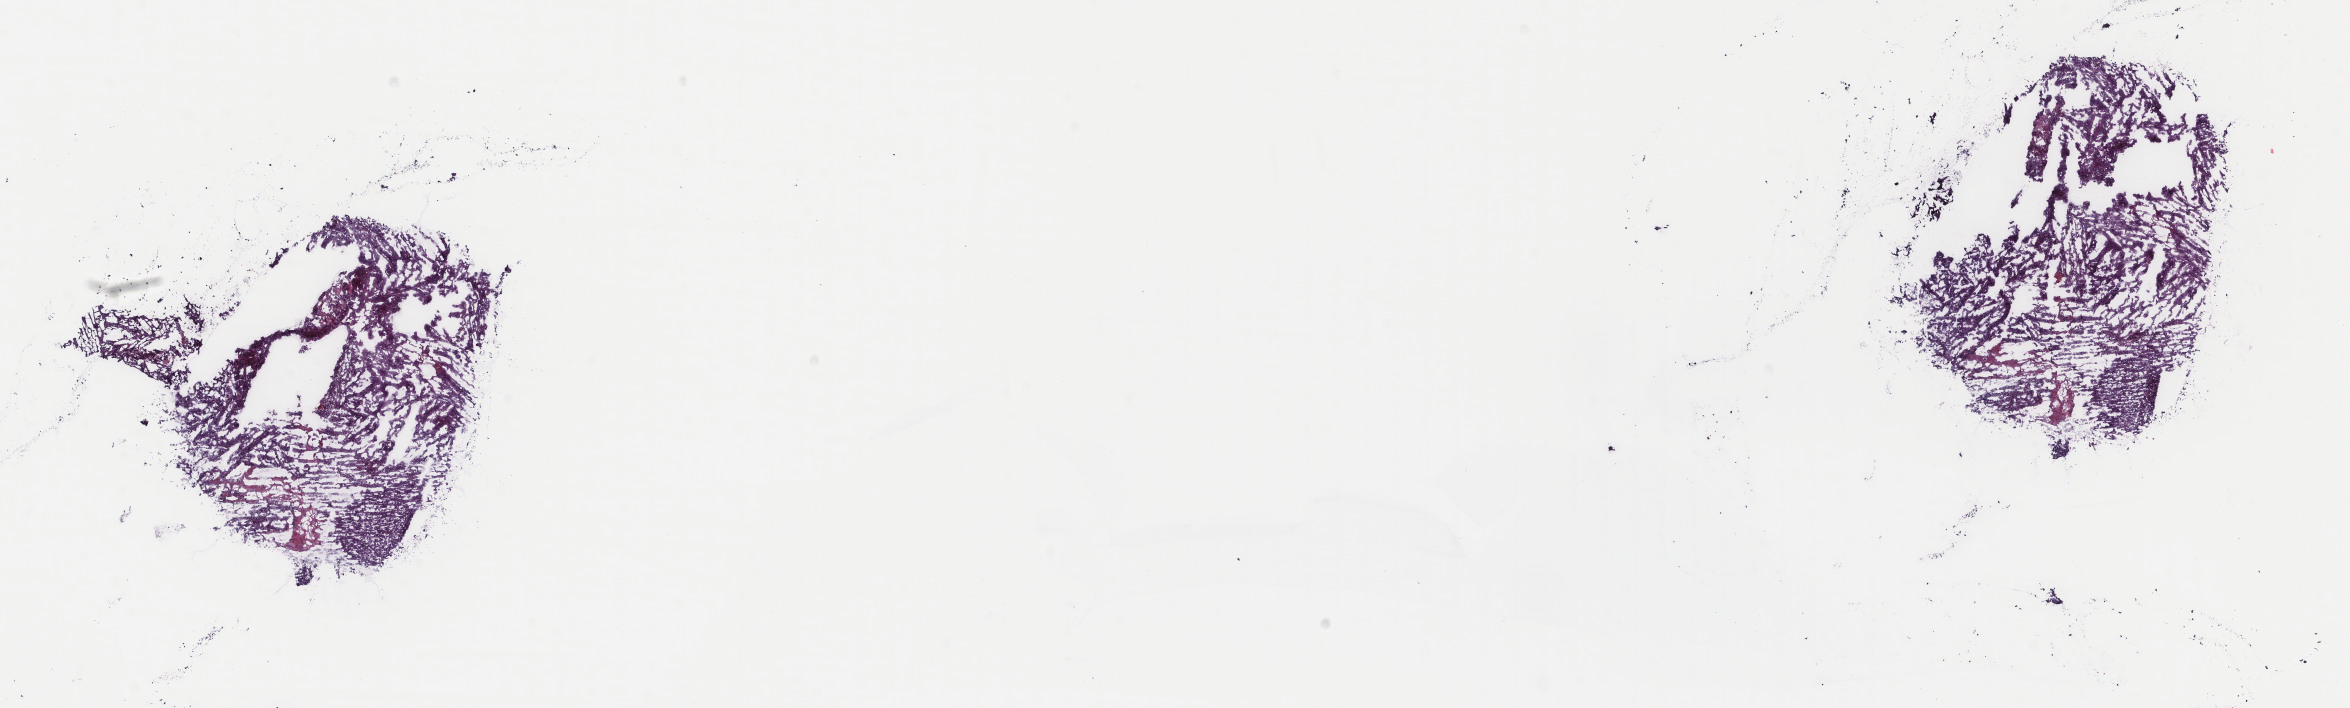
Hematoxylin and eosin (H&E) stained whole-slide image, low-resolution overview of the scanned area, about 18.7 x 5.6 mm (acquisition: 40x scan), frozen section, adrenal cortex, primary tumour sample. Male patient; age at initial diagnosis 42 years. Slide review estimates, as recorded: tumour cells 100%, tumour nuclei 80%, normal cells 0%, stromal cells 0%, necrosis 0%. Infiltration values recorded for this section: lymphocyte infiltration 1%, monocyte infiltration 0%, neutrophil infiltration 0%.
• histologic diagnosis: Adrenal cortical carcinoma (cortex of adrenal gland)